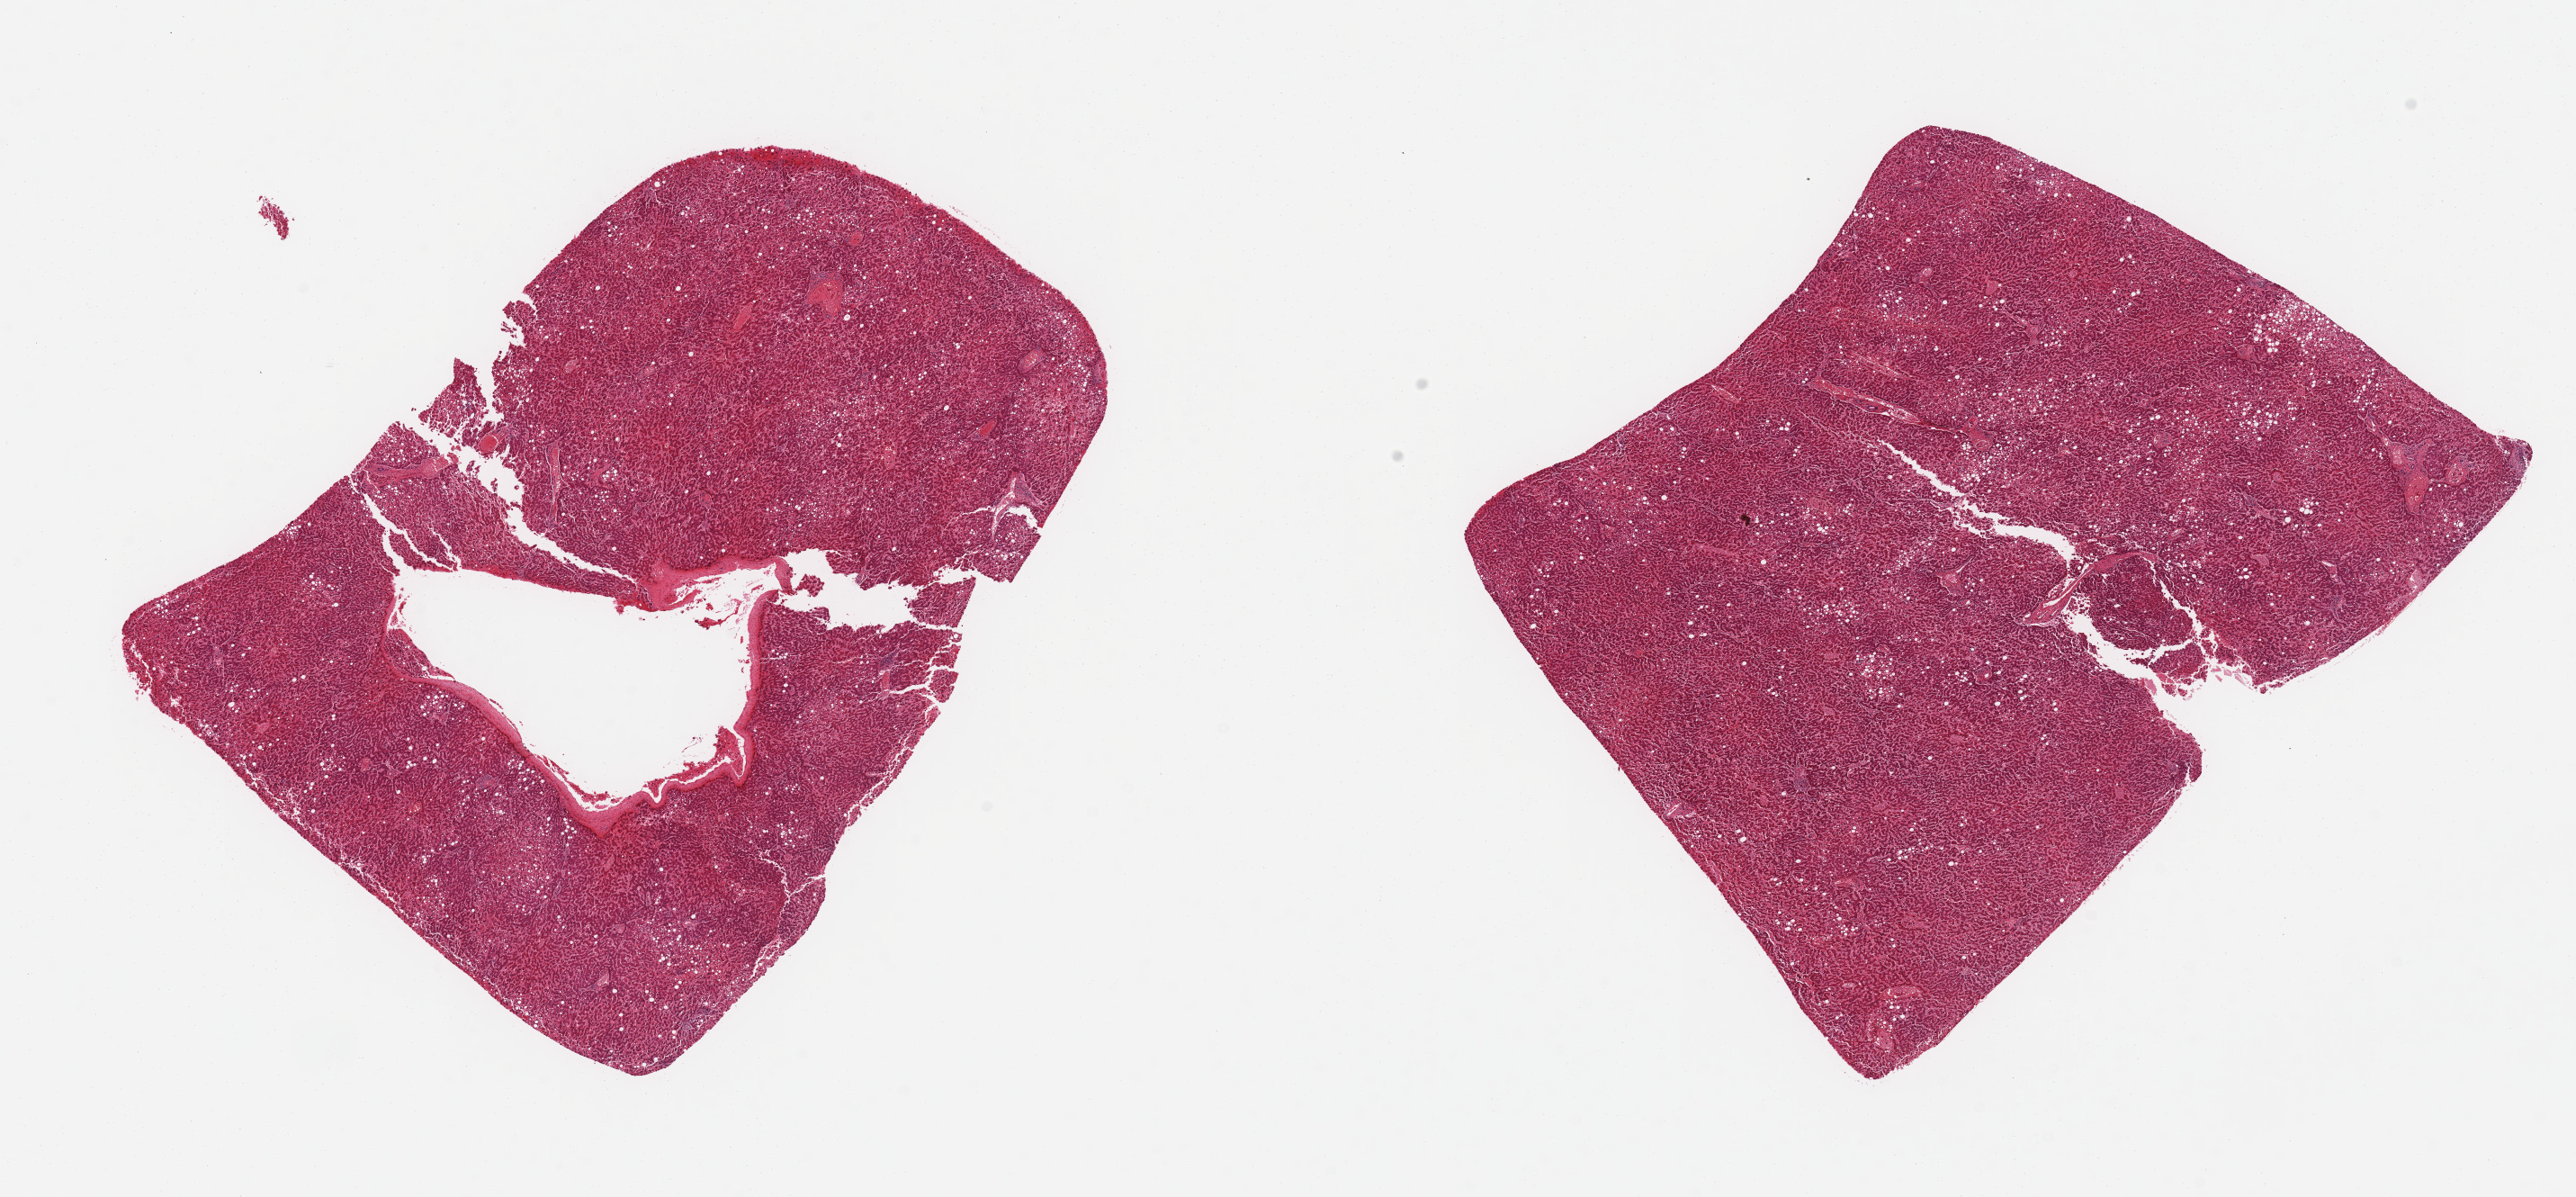
Whole-slide image, haematoxylin and eosin stain — low-resolution overview of the scanned area, about 22.6 x 10.5 mm, PAXgene-fixed paraffin-embedded (PFPE) section, section of liver (target tissue), tissue donor sample. Male donor.
Review note (as recorded): 2 pieces, patchy macrovesicular steatosis involves ~20% of parenchyma.